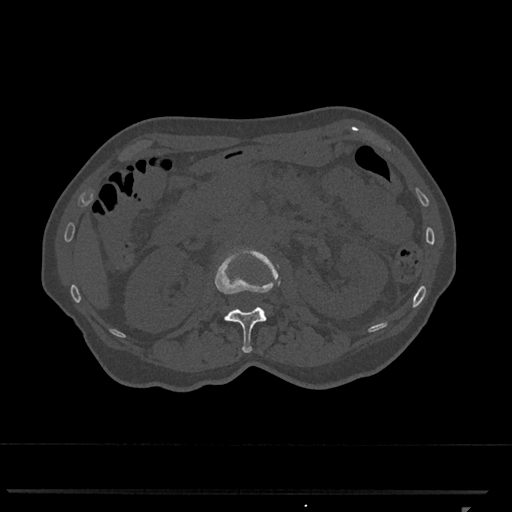
CT including the spine, one axial slice. Slice 386 of 793 in the series (ordered by position). Reconstruction kernel Br40s/3. 120 kVp. Bone window (W 1800 / L 400 HU). 512 × 512 image matrix, field of view 380 × 380 mm. Female patient, age 62 years. Case-level facts recorded for this patient, not image findings: primary cancer: renal.
Annotated regions visible in this slice (semi-automatically segmented with operator editing):
- L1 vertebra: bounding box [x1, y1, x2, y2] px = [215, 248, 281, 353]